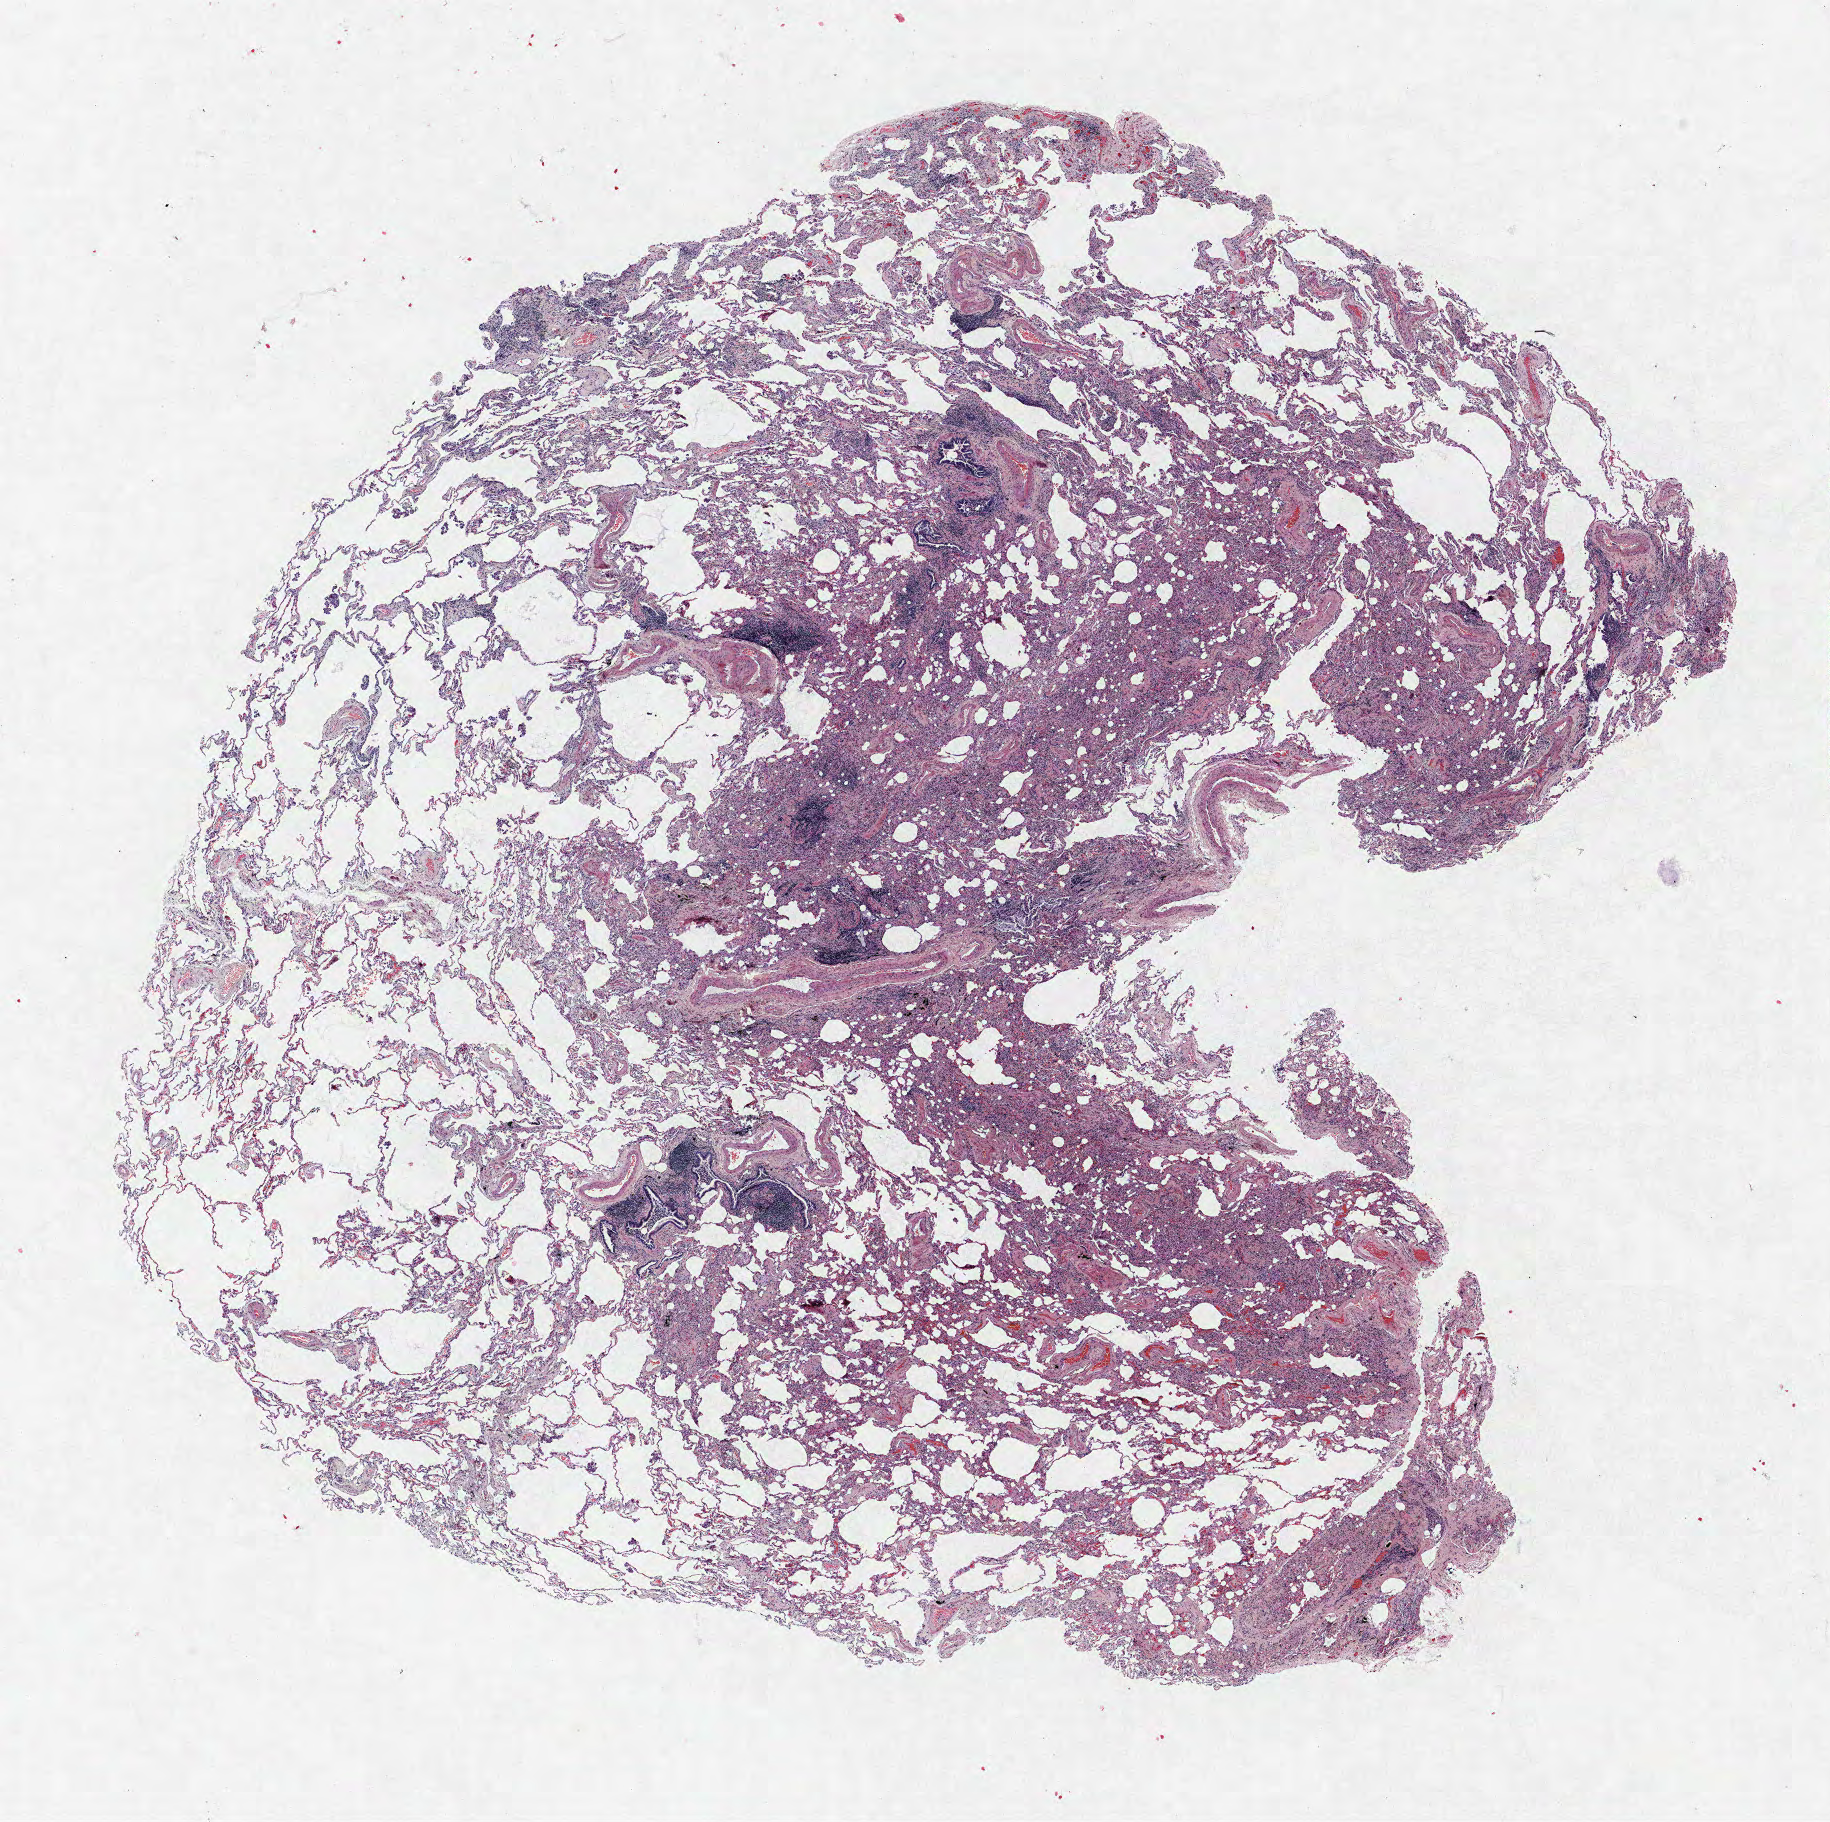
Whole-slide histology image, H&E-stained — a low-resolution overview of the entire scanned area, about 14.6 x 14.6 mm (from a 40x scan). FFPE section. Lung. Male, age 73 at enrolment. Grade: well differentiated (G1).
- participant's lung-cancer diagnosis: Adenocarcinoma, NOS
- primary tumour location (clinical record): right lower lobe
- ICD-O-3 topography: lower lobe of lung (C34.3)
- stage (AJCC 6th edition): IA
- tumour size (pathology): 18 mm